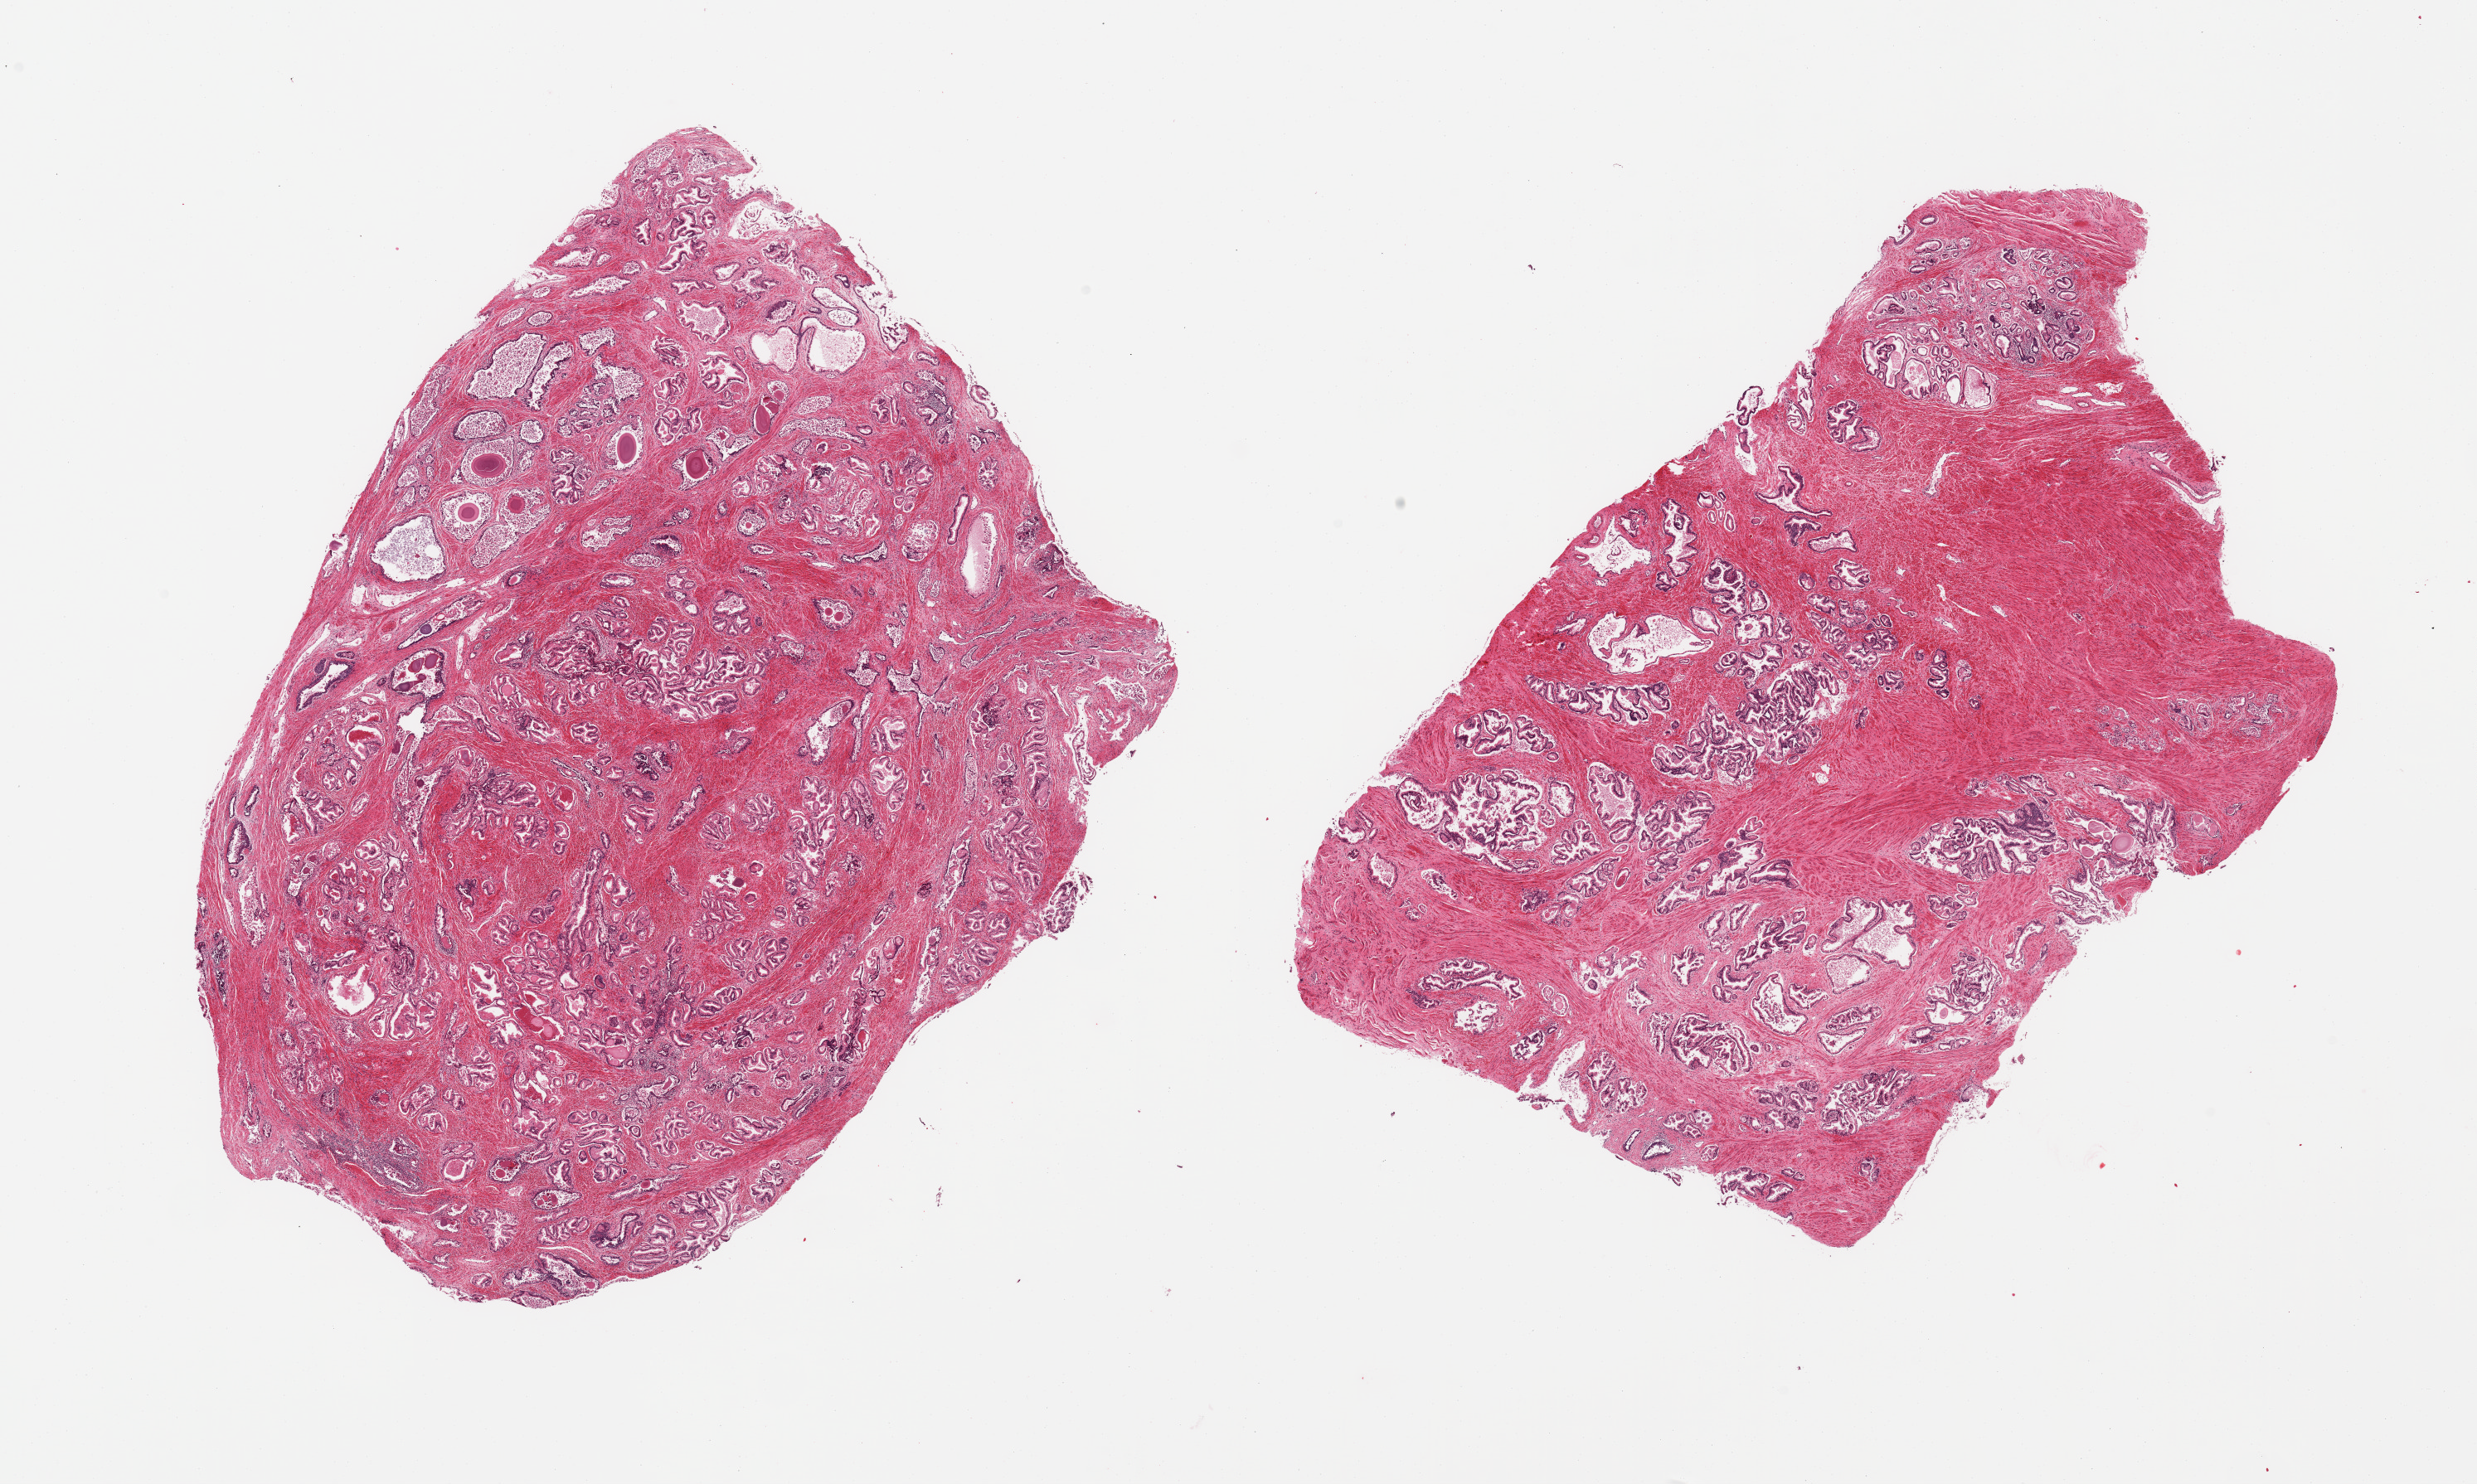
Digitized H&E-stained section — whole scanned area (about 23.6 x 14.2 mm) shown as a low-resolution overview; PAXgene-fixed paraffin-embedded (PFPE) section; sampled site (target tissue): prostate; donor tissue sample.
Pathologist's review note for this sample: 2 pieces, hyperplastic glandular pattern, epithelium averages moderately advanced autolysis.